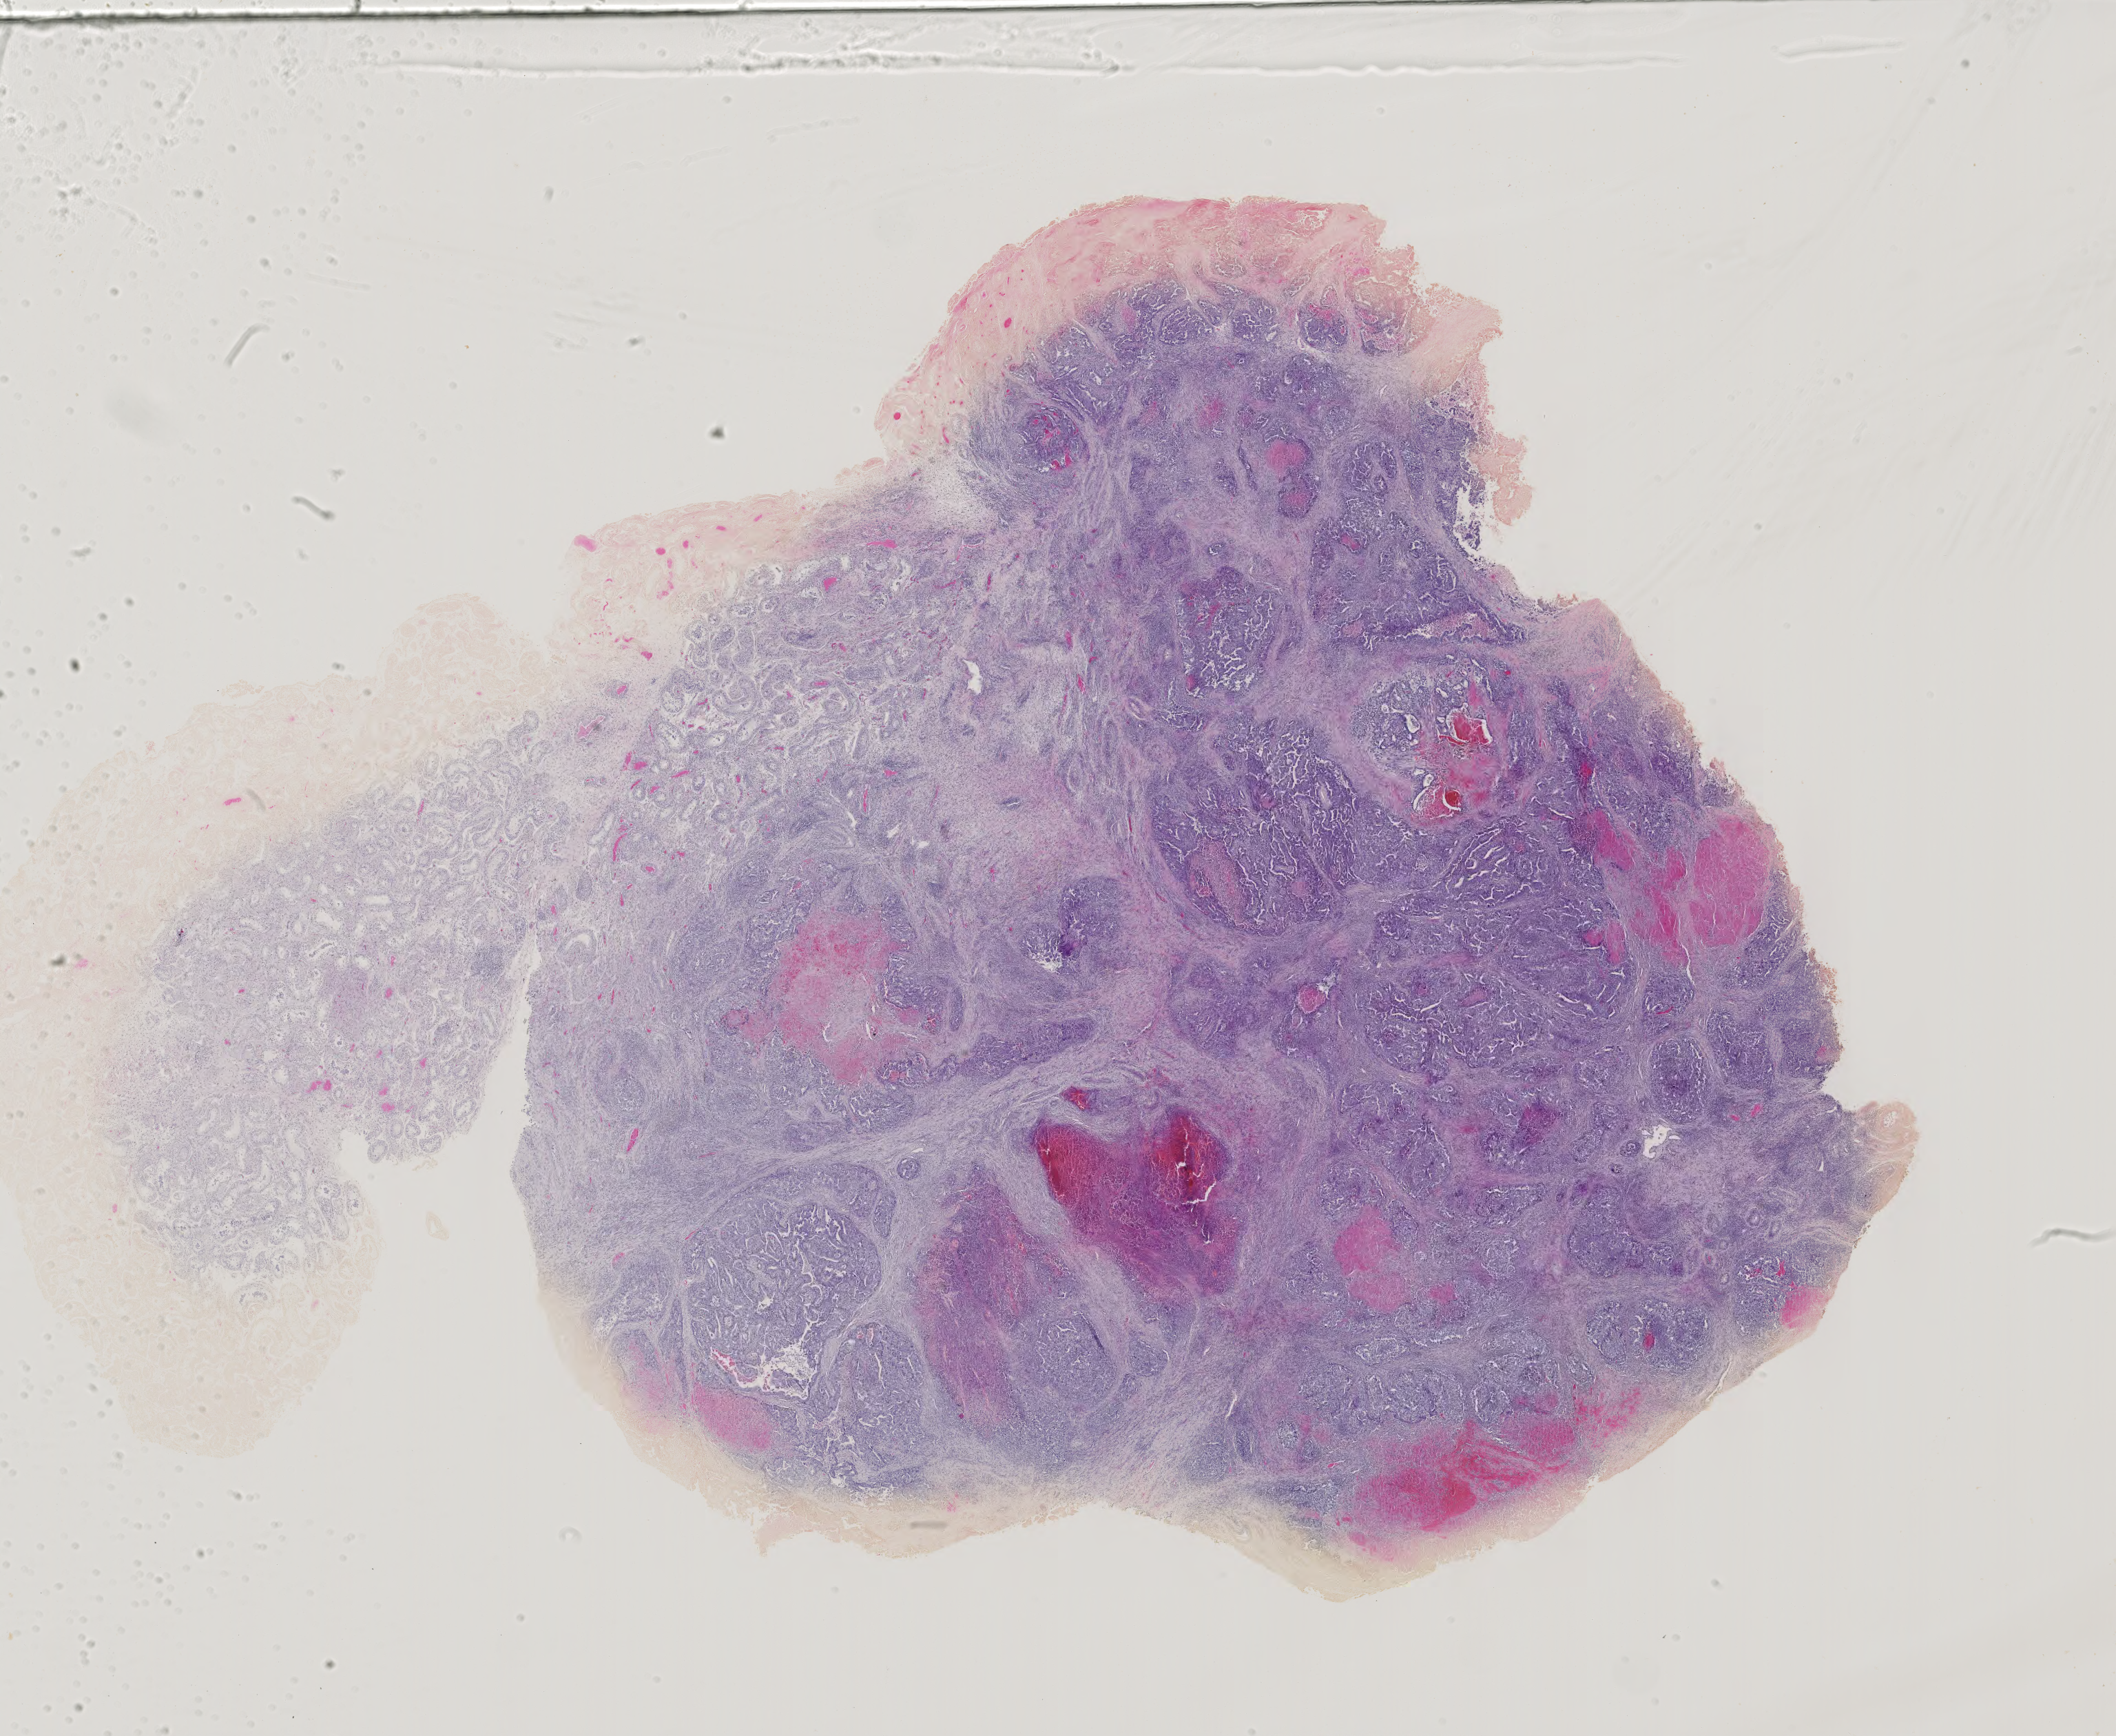
Digitized H&E tissue section (whole slide), whole scanned area (about 22.4 x 18.4 mm, slide scanned at 40x) shown as a low-resolution overview; FFPE section; sample: primary tumour, testis. Male, age 18 years at initial diagnosis.
• AJCC pathologic stage: III (4th edition)
• laterality: right
• TNM: T2 NX M0
• histologic diagnosis: Embryonal carcinoma, NOS